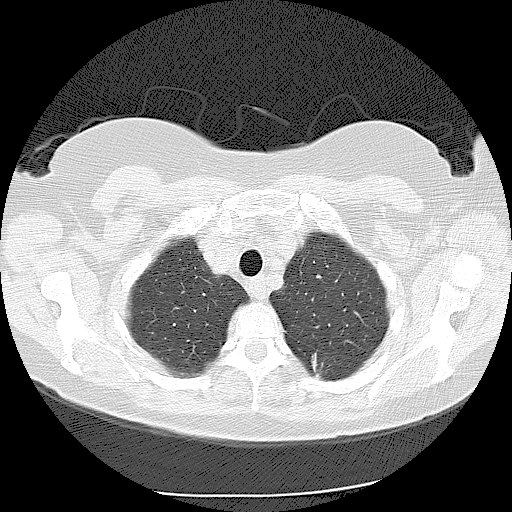
Low-dose screening chest CT, one axial slice; slice 95 of 116 in the series (ordered by position); 120 kVp; lung window (W 1500 / L -600 HU); 2.5 mm slice thickness; 512 × 512 image matrix, field of view 360 × 360 mm.
Structures marked on this image (manually delineated by an expert):
- lesion 1 (tumor, lower lobe of left lung): box from (x=311, y=353) to (x=324, y=379) px